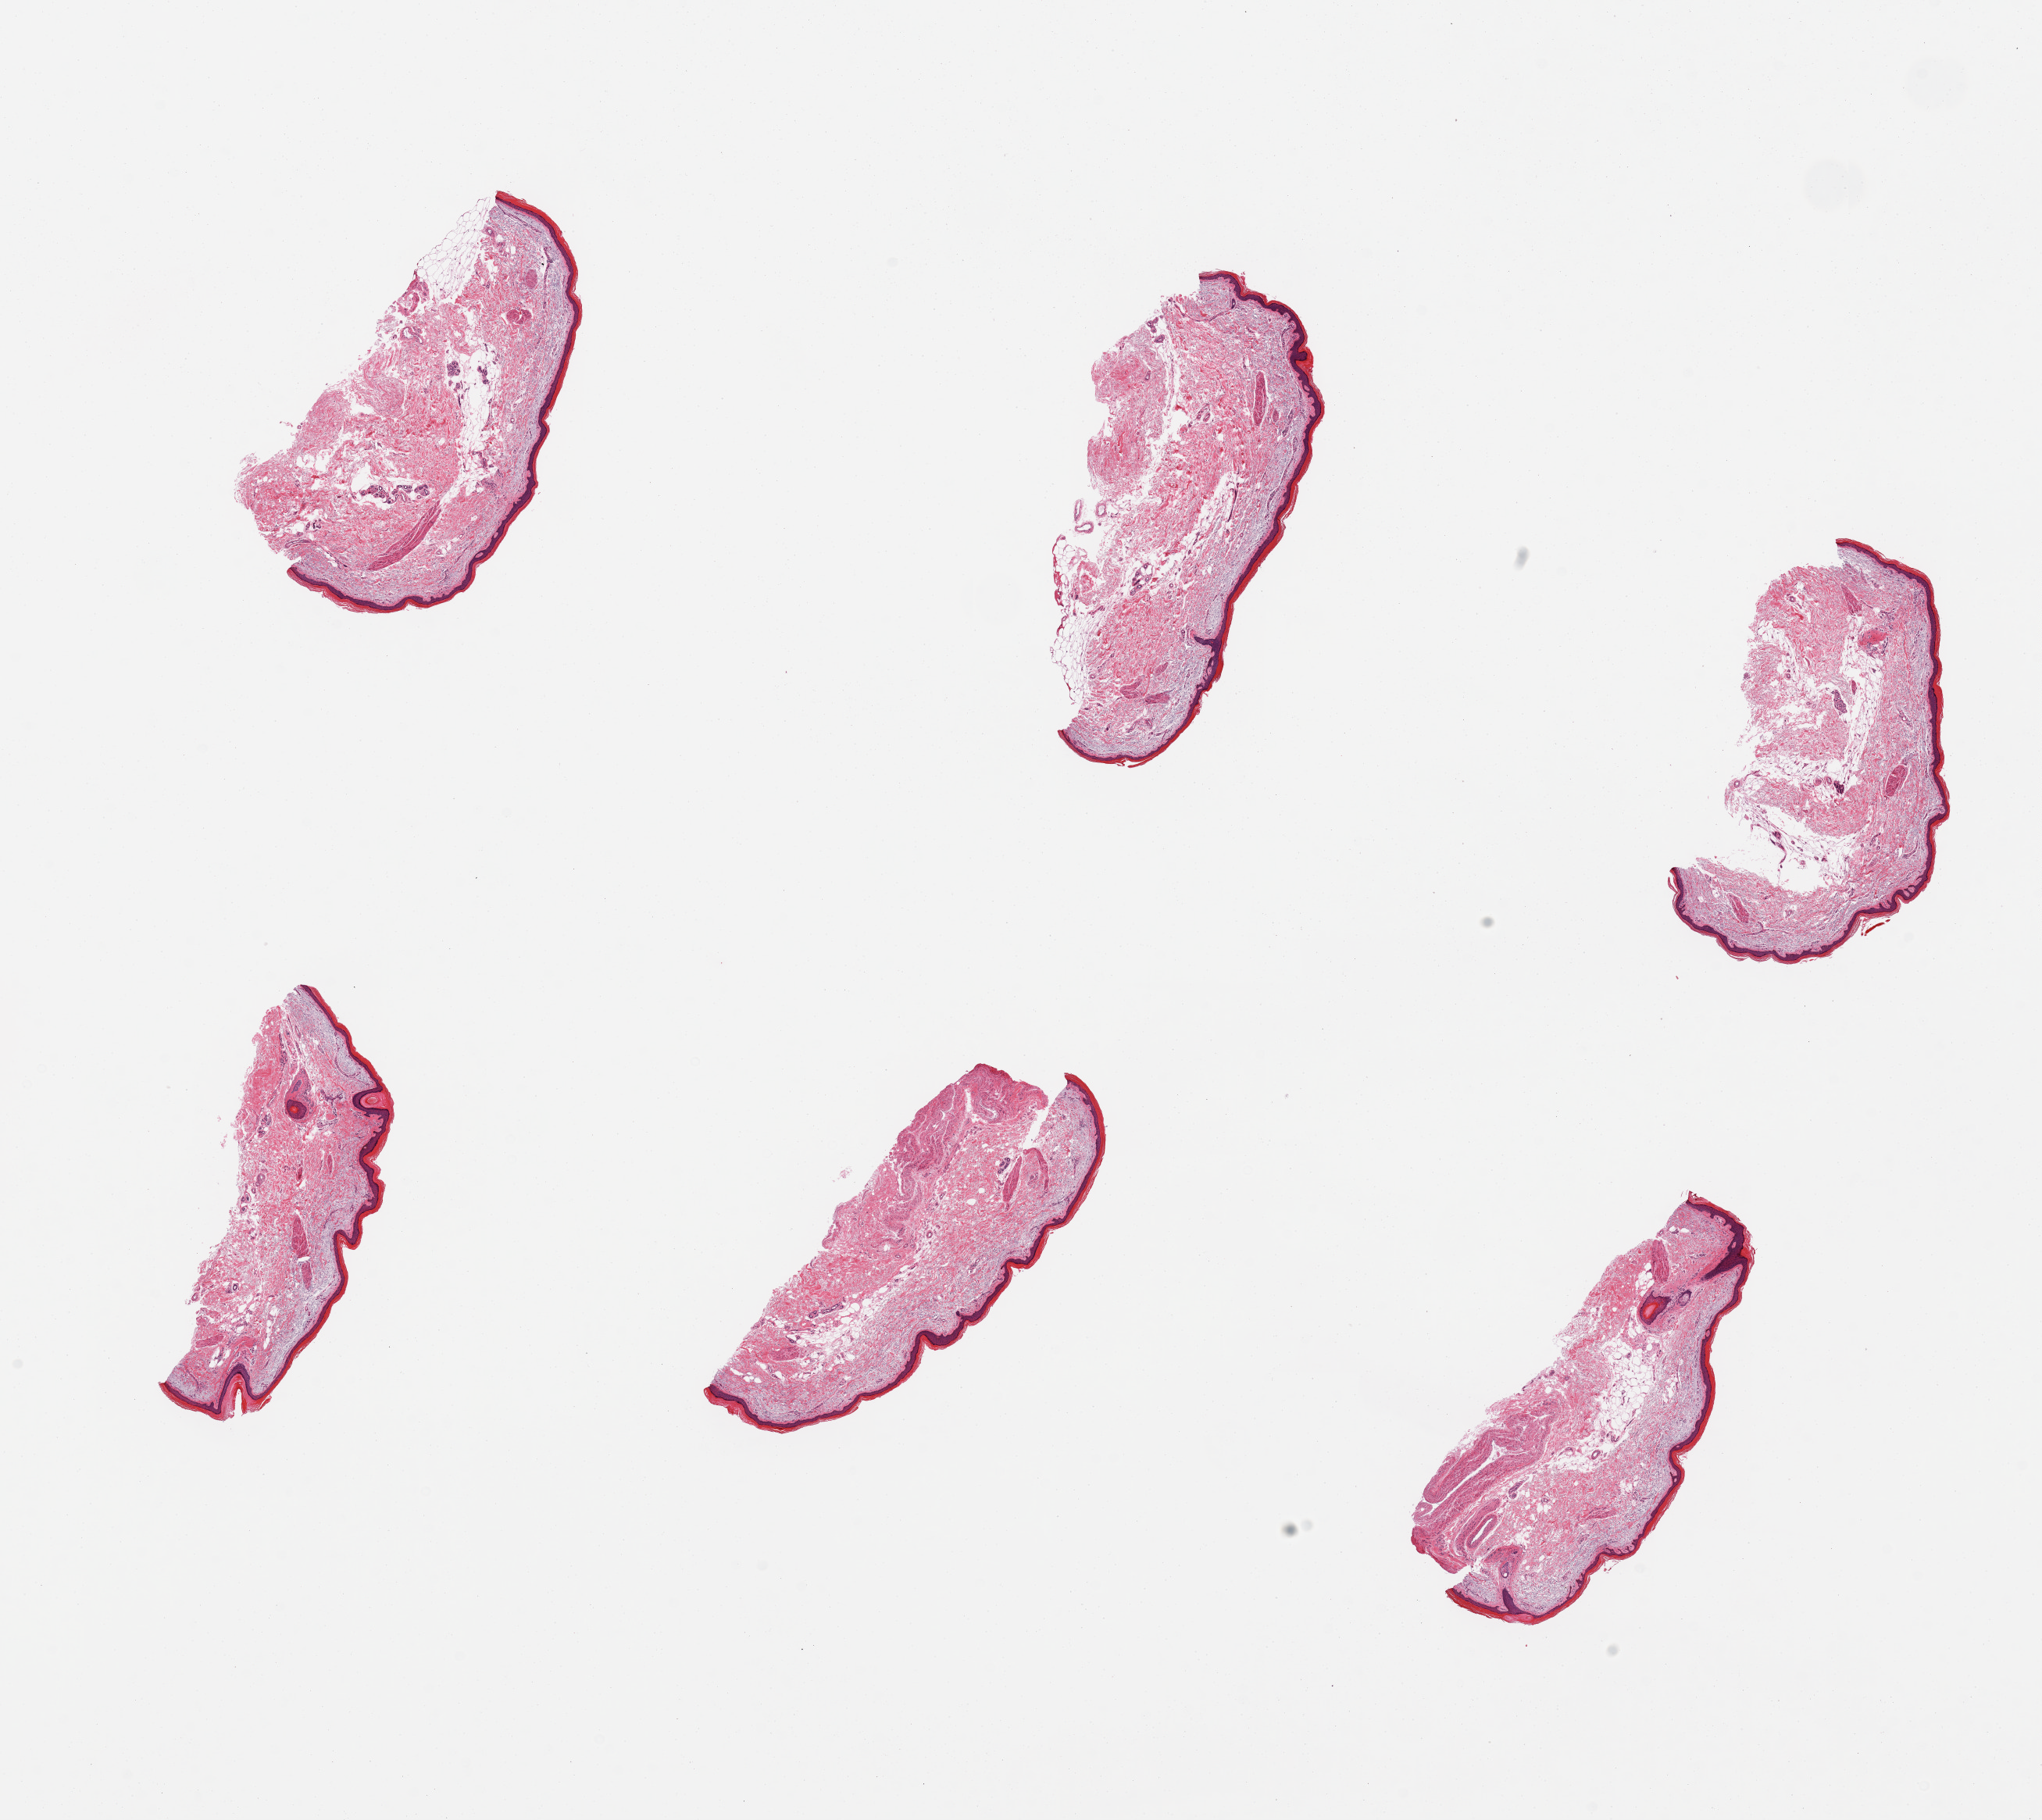
Whole-slide image, haematoxylin and eosin stain, a low-resolution overview of the entire scanned area, about 20.7 x 18.4 mm (acquisition: 20x scan), PAXgene-fixed paraffin-embedded (PFPE) section, section of skin of lower leg (target tissue), tissue donor sample. Donor: female.
Reviewer comment on this tissue sample: 6 pieces; well dissected.